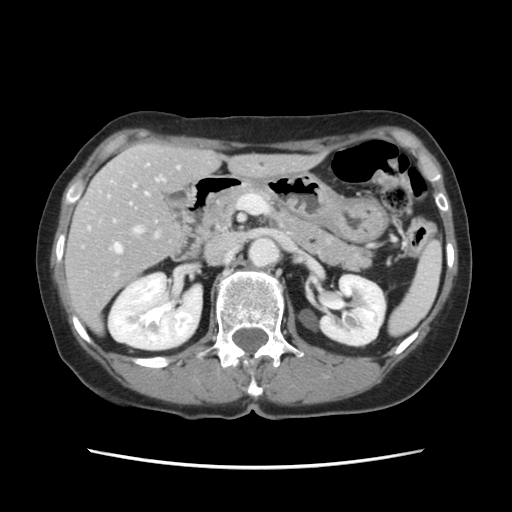
Contrast-enhanced abdominal CT, one axial slice; slice 63 of 120 in the series (ordered by position); 120 kVp; intravenous contrast given; soft-tissue window (W 400 / L 40 HU); 2.5 mm slice thickness; 512 × 512 image matrix. Female patient, age 70 years. Case-level facts recorded for this patient, not image findings: diagnosis: colorectal cancer liver metastases, imaged before liver resection; multiple liver metastases: no; largest metastasis: 2.5 cm.
Outlined on this slice (manually delineated by an expert):
- hepatic veins: bounding box <88,177,164,253> (left, top, right, bottom; pixels)
- liver: <67,144,316,328>
- planned liver remnant (the part of the liver to remain after resection): <74,144,317,281>
- portal vein (with intrahepatic branches): <108,166,179,237>